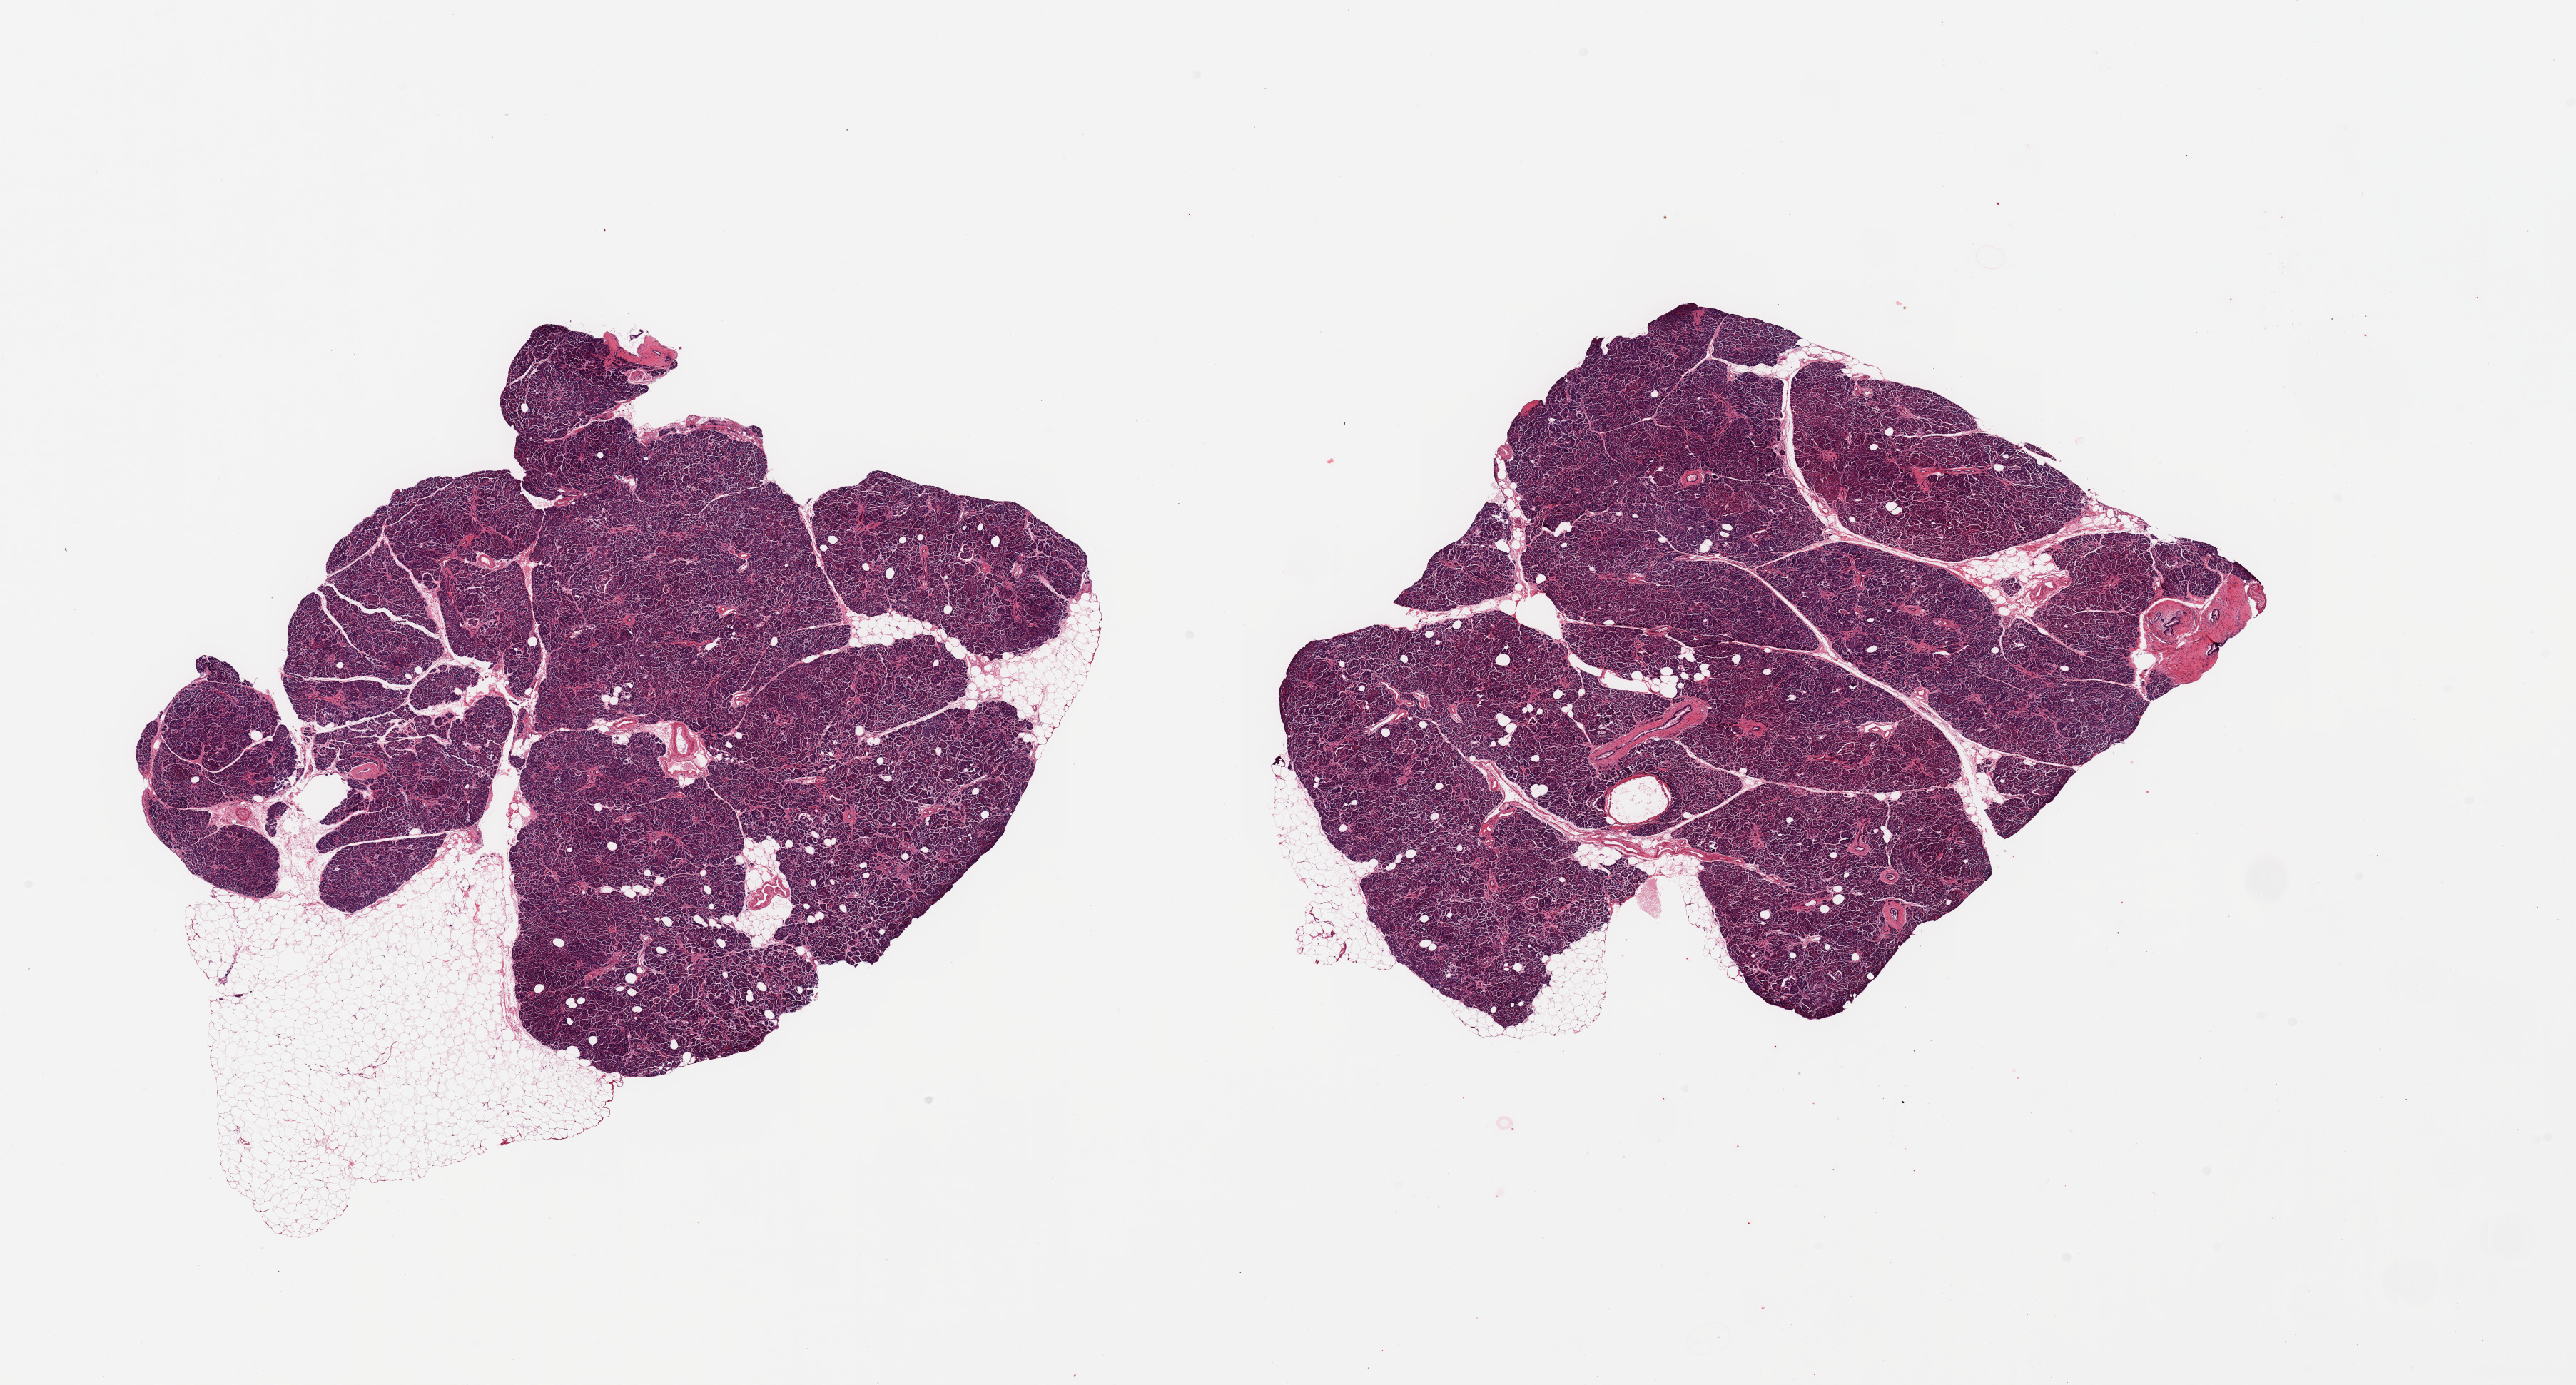
Whole-slide image, H&E stain — a low-resolution overview of the entire scanned area, about 28.5 x 15.3 mm, PAXgene-fixed paraffin-embedded (PFPE) section, section of pancreas (target tissue), tissue donor sample. Donor sex: male.
Pathologist's review note for this sample: 2 pieces; PanIN 1A lesions in 1 labeled focus. 5% internal fat.